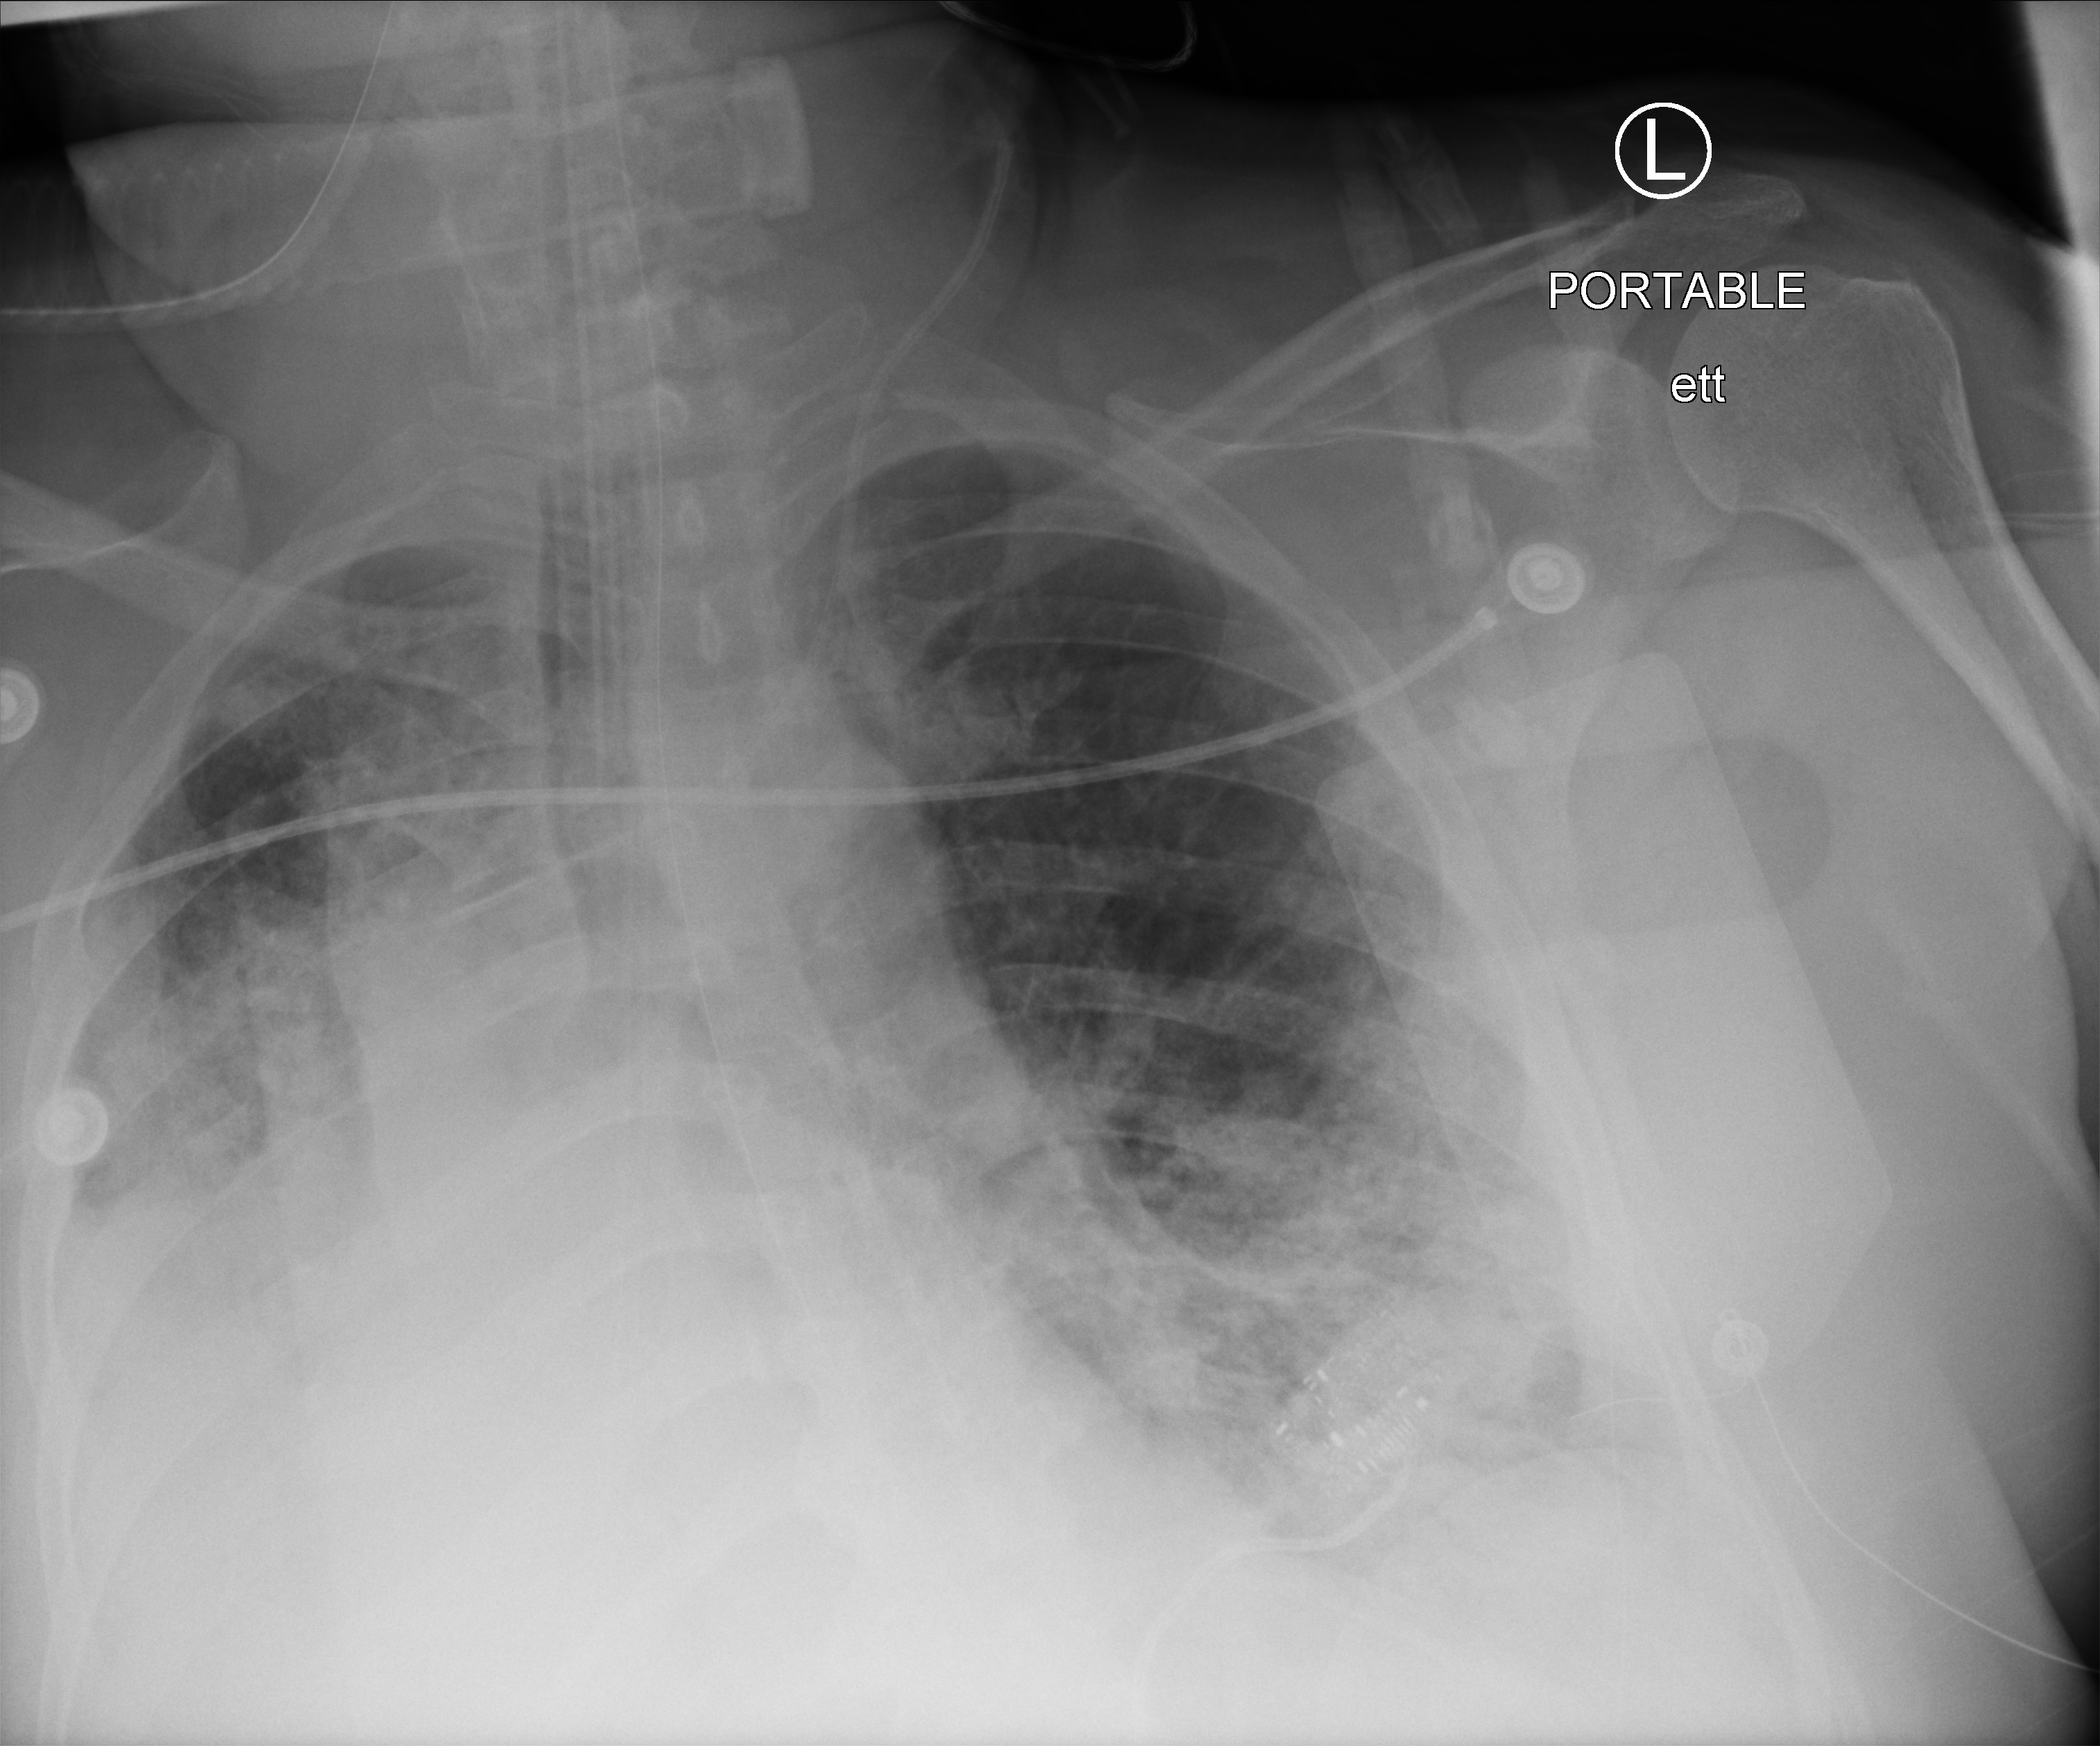
Portable chest radiograph; anteroposterior (AP) projection. Patient hospitalised with COVID-19, aged 18–59 years.
Admission-level facts for this patient (not findings on this image; timing relative to this image not recorded):
- length of hospital stay: 13 days
- mechanically ventilated during this hospital stay: yes
- admitted to intensive care during this hospital stay: yes